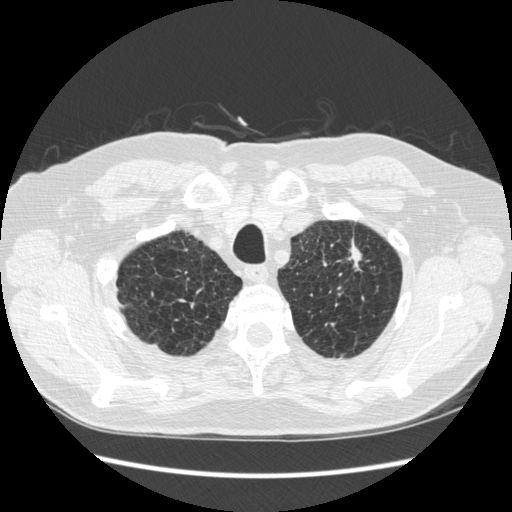
Low-dose screening chest CT, axial slice. Third annual screen. Lung window (W 1500 / L -600 HU). 1.25 mm slice thickness. Slice 35 of 267 in the series. Male, age 70 years at enrolment.
- Expert-annotated lung lesion, bounding box [x1, y1, x2, y2] px = [324, 229, 378, 294].
- The screening reader recorded 2 non-calcified nodules or masses ≥4 mm on this exam (left upper lobe, right lower lobe); which of them this box marks is not recorded.
- Official screen result: positive, other.